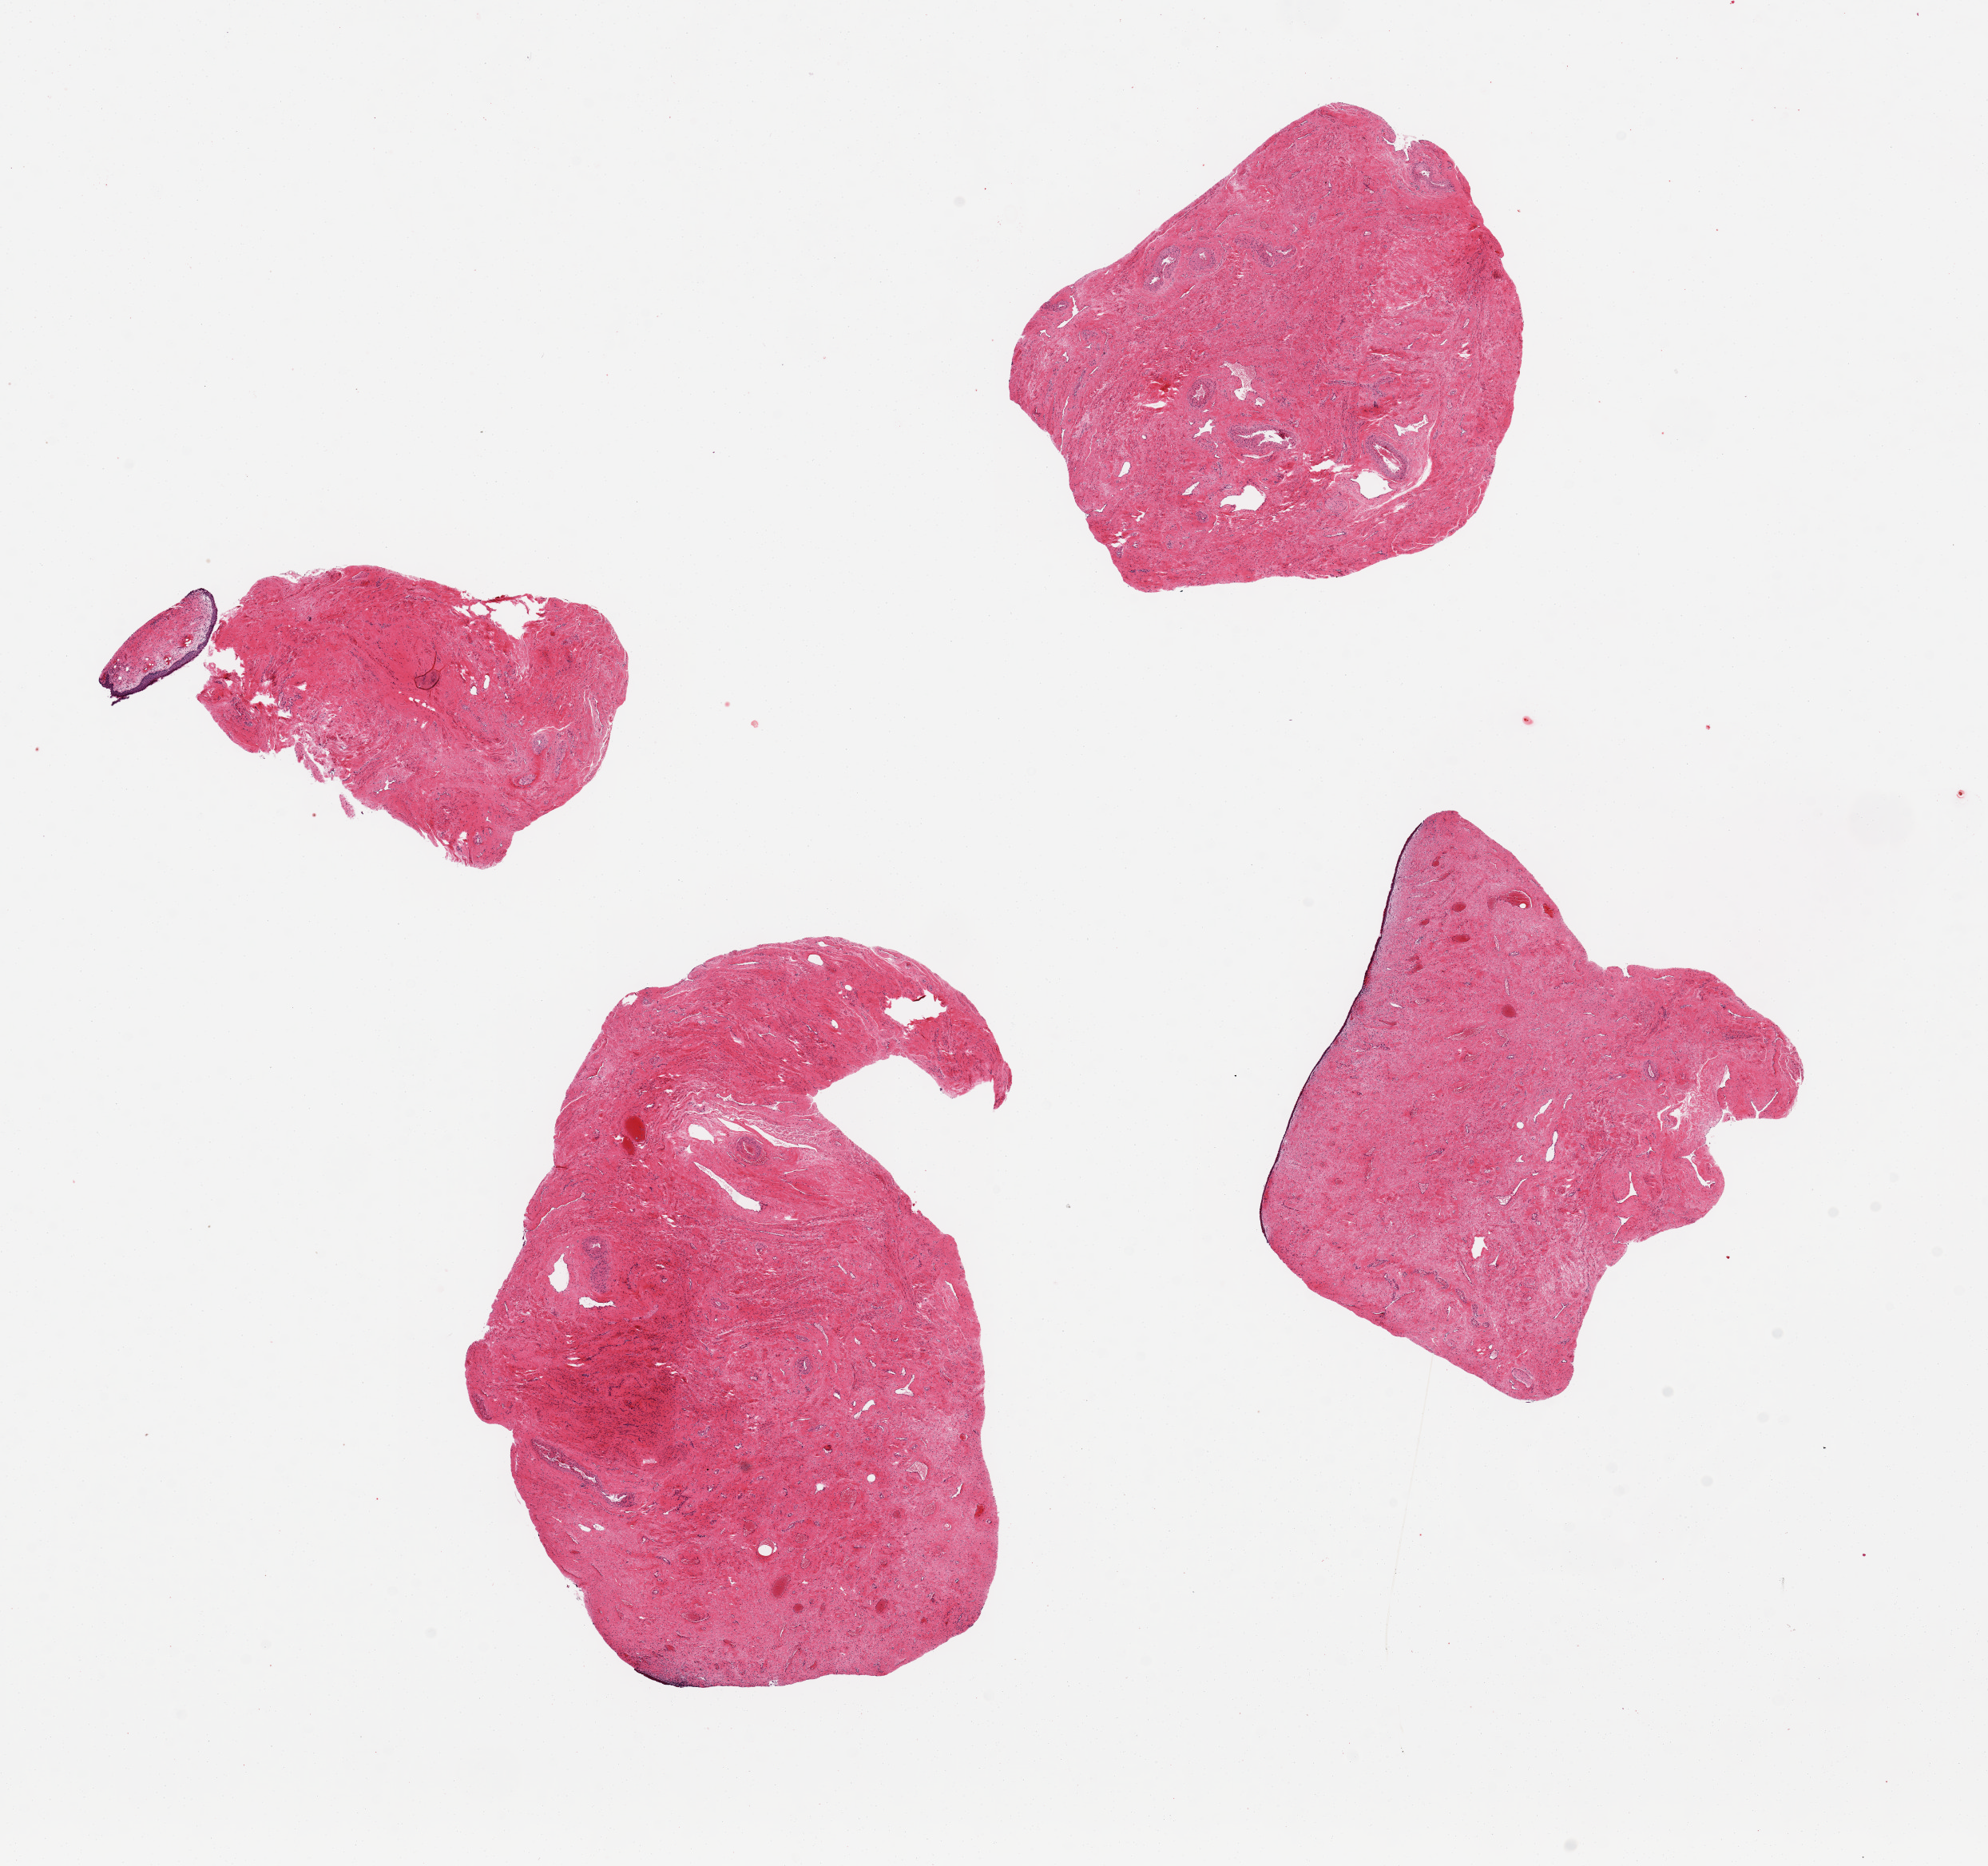
Digitized hematoxylin and eosin (H&E)-stained section, brightfield, shown as a low-resolution overview of the whole scanned area (about 19.7 x 18.5 mm), PAXgene-fixed, paraffin-embedded tissue, target tissue: exocervix, donor tissue sample. Donor: female.
* pathologist's review note for this sample: 4 pieces, ~4x4mm. 2 have atrophic squamous mucosa, <<1% of thickness